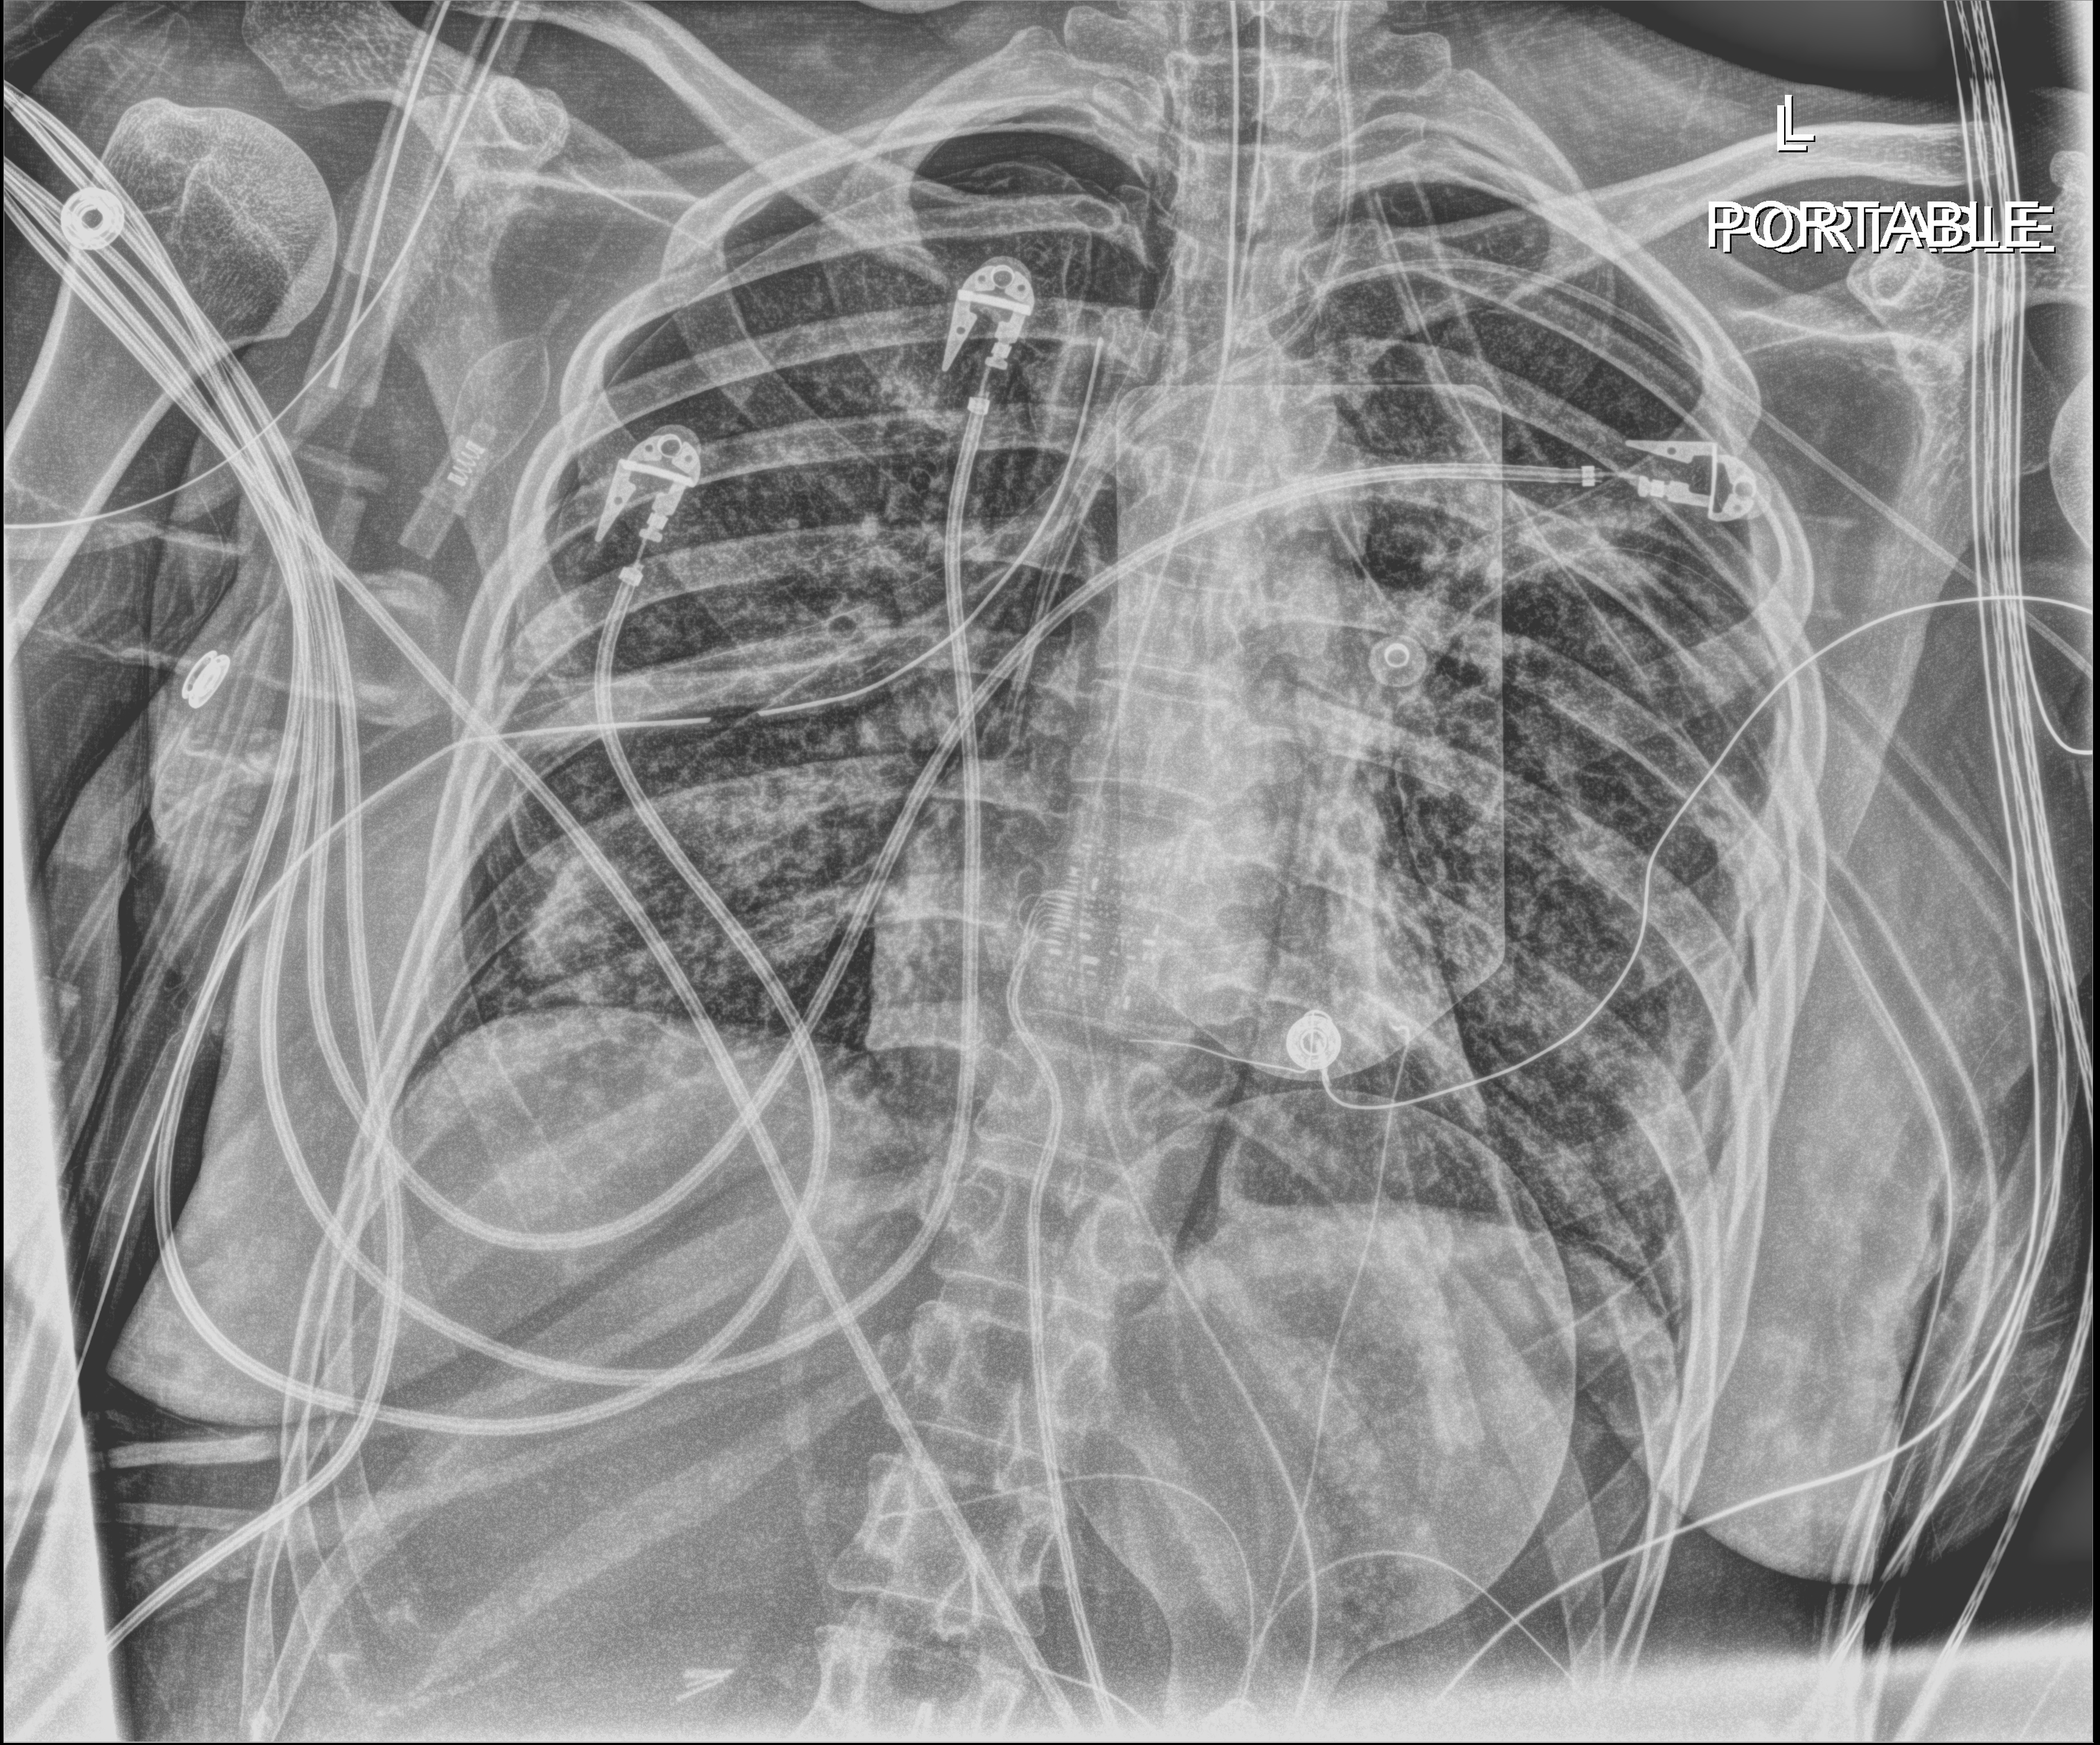
Chest X-ray (portable). Patient hospitalised with COVID-19, aged 18–59 years.
Admission-level facts for this patient (not findings on this image; timing relative to this image not recorded):
- mechanically ventilated during this hospital stay: yes
- admitted to intensive care during this hospital stay: yes
- other chronic lung disease (admission record): no